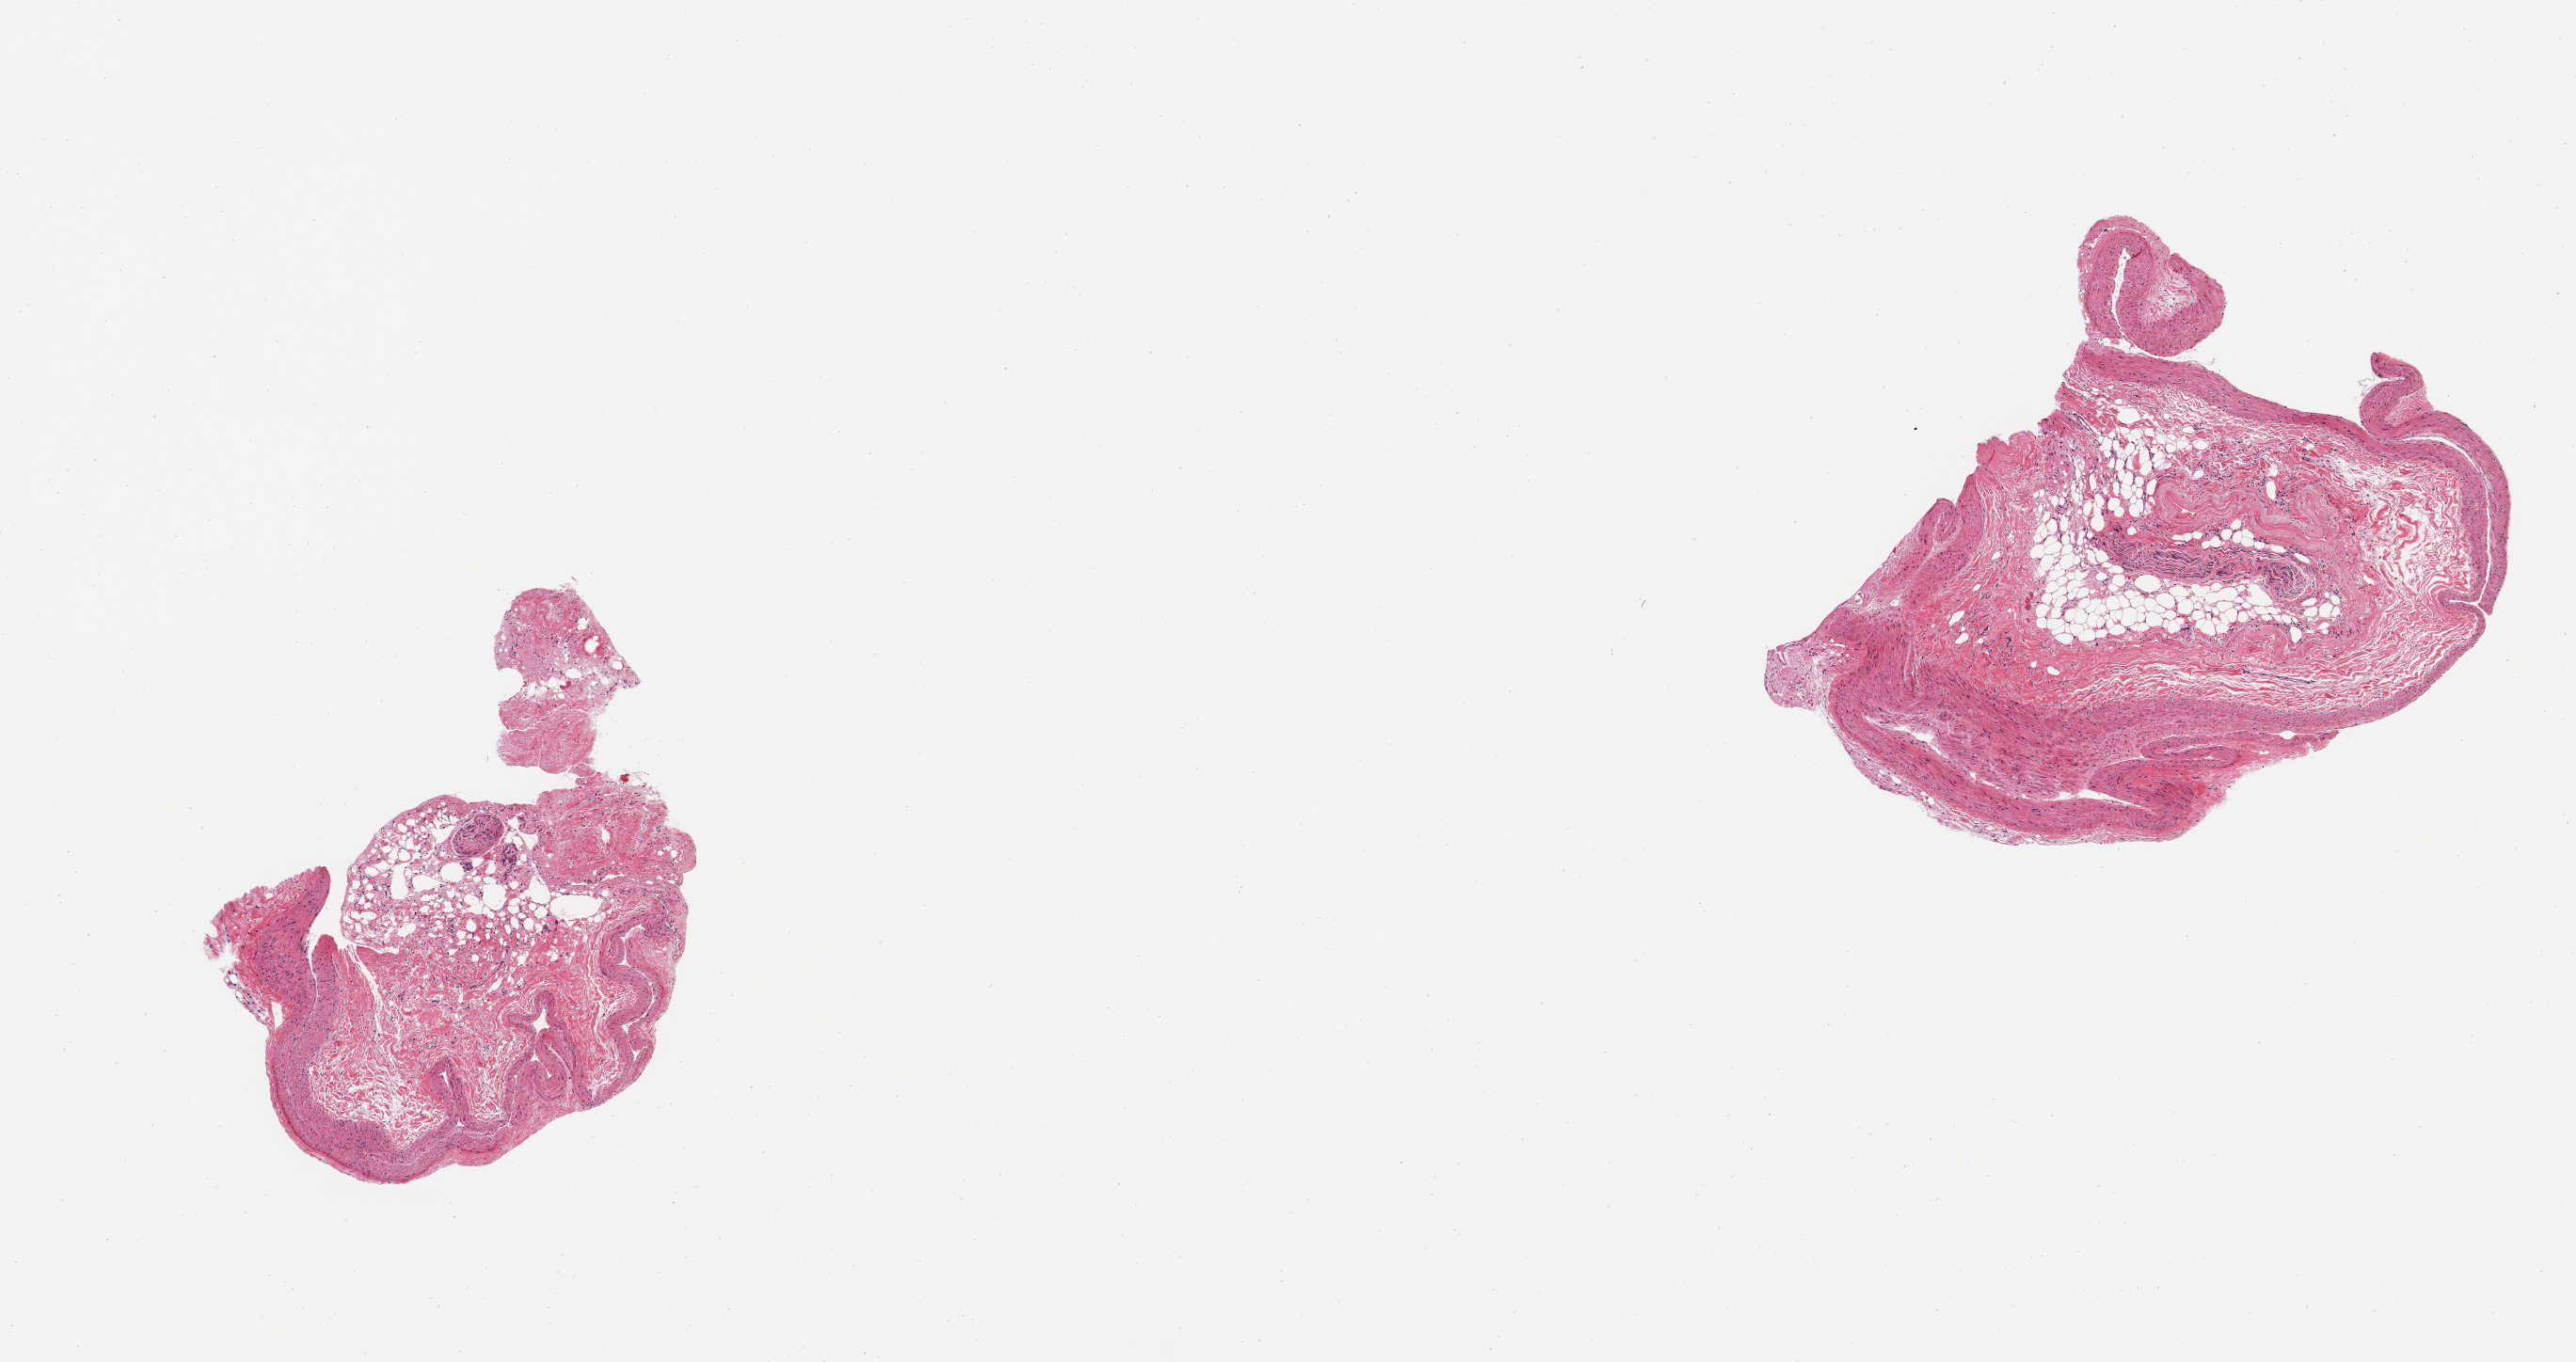
Haematoxylin and eosin whole-slide image — a low-resolution overview of the entire scanned area, about 10.8 x 5.7 mm (from a 20x scan); PAXgene-fixed, paraffin-embedded tissue; sampled site (target tissue): coronary artery; tissue donor sample.
- pathologist's review note for this sample: 2 pieces; specimen is up to 70% fat and nerve